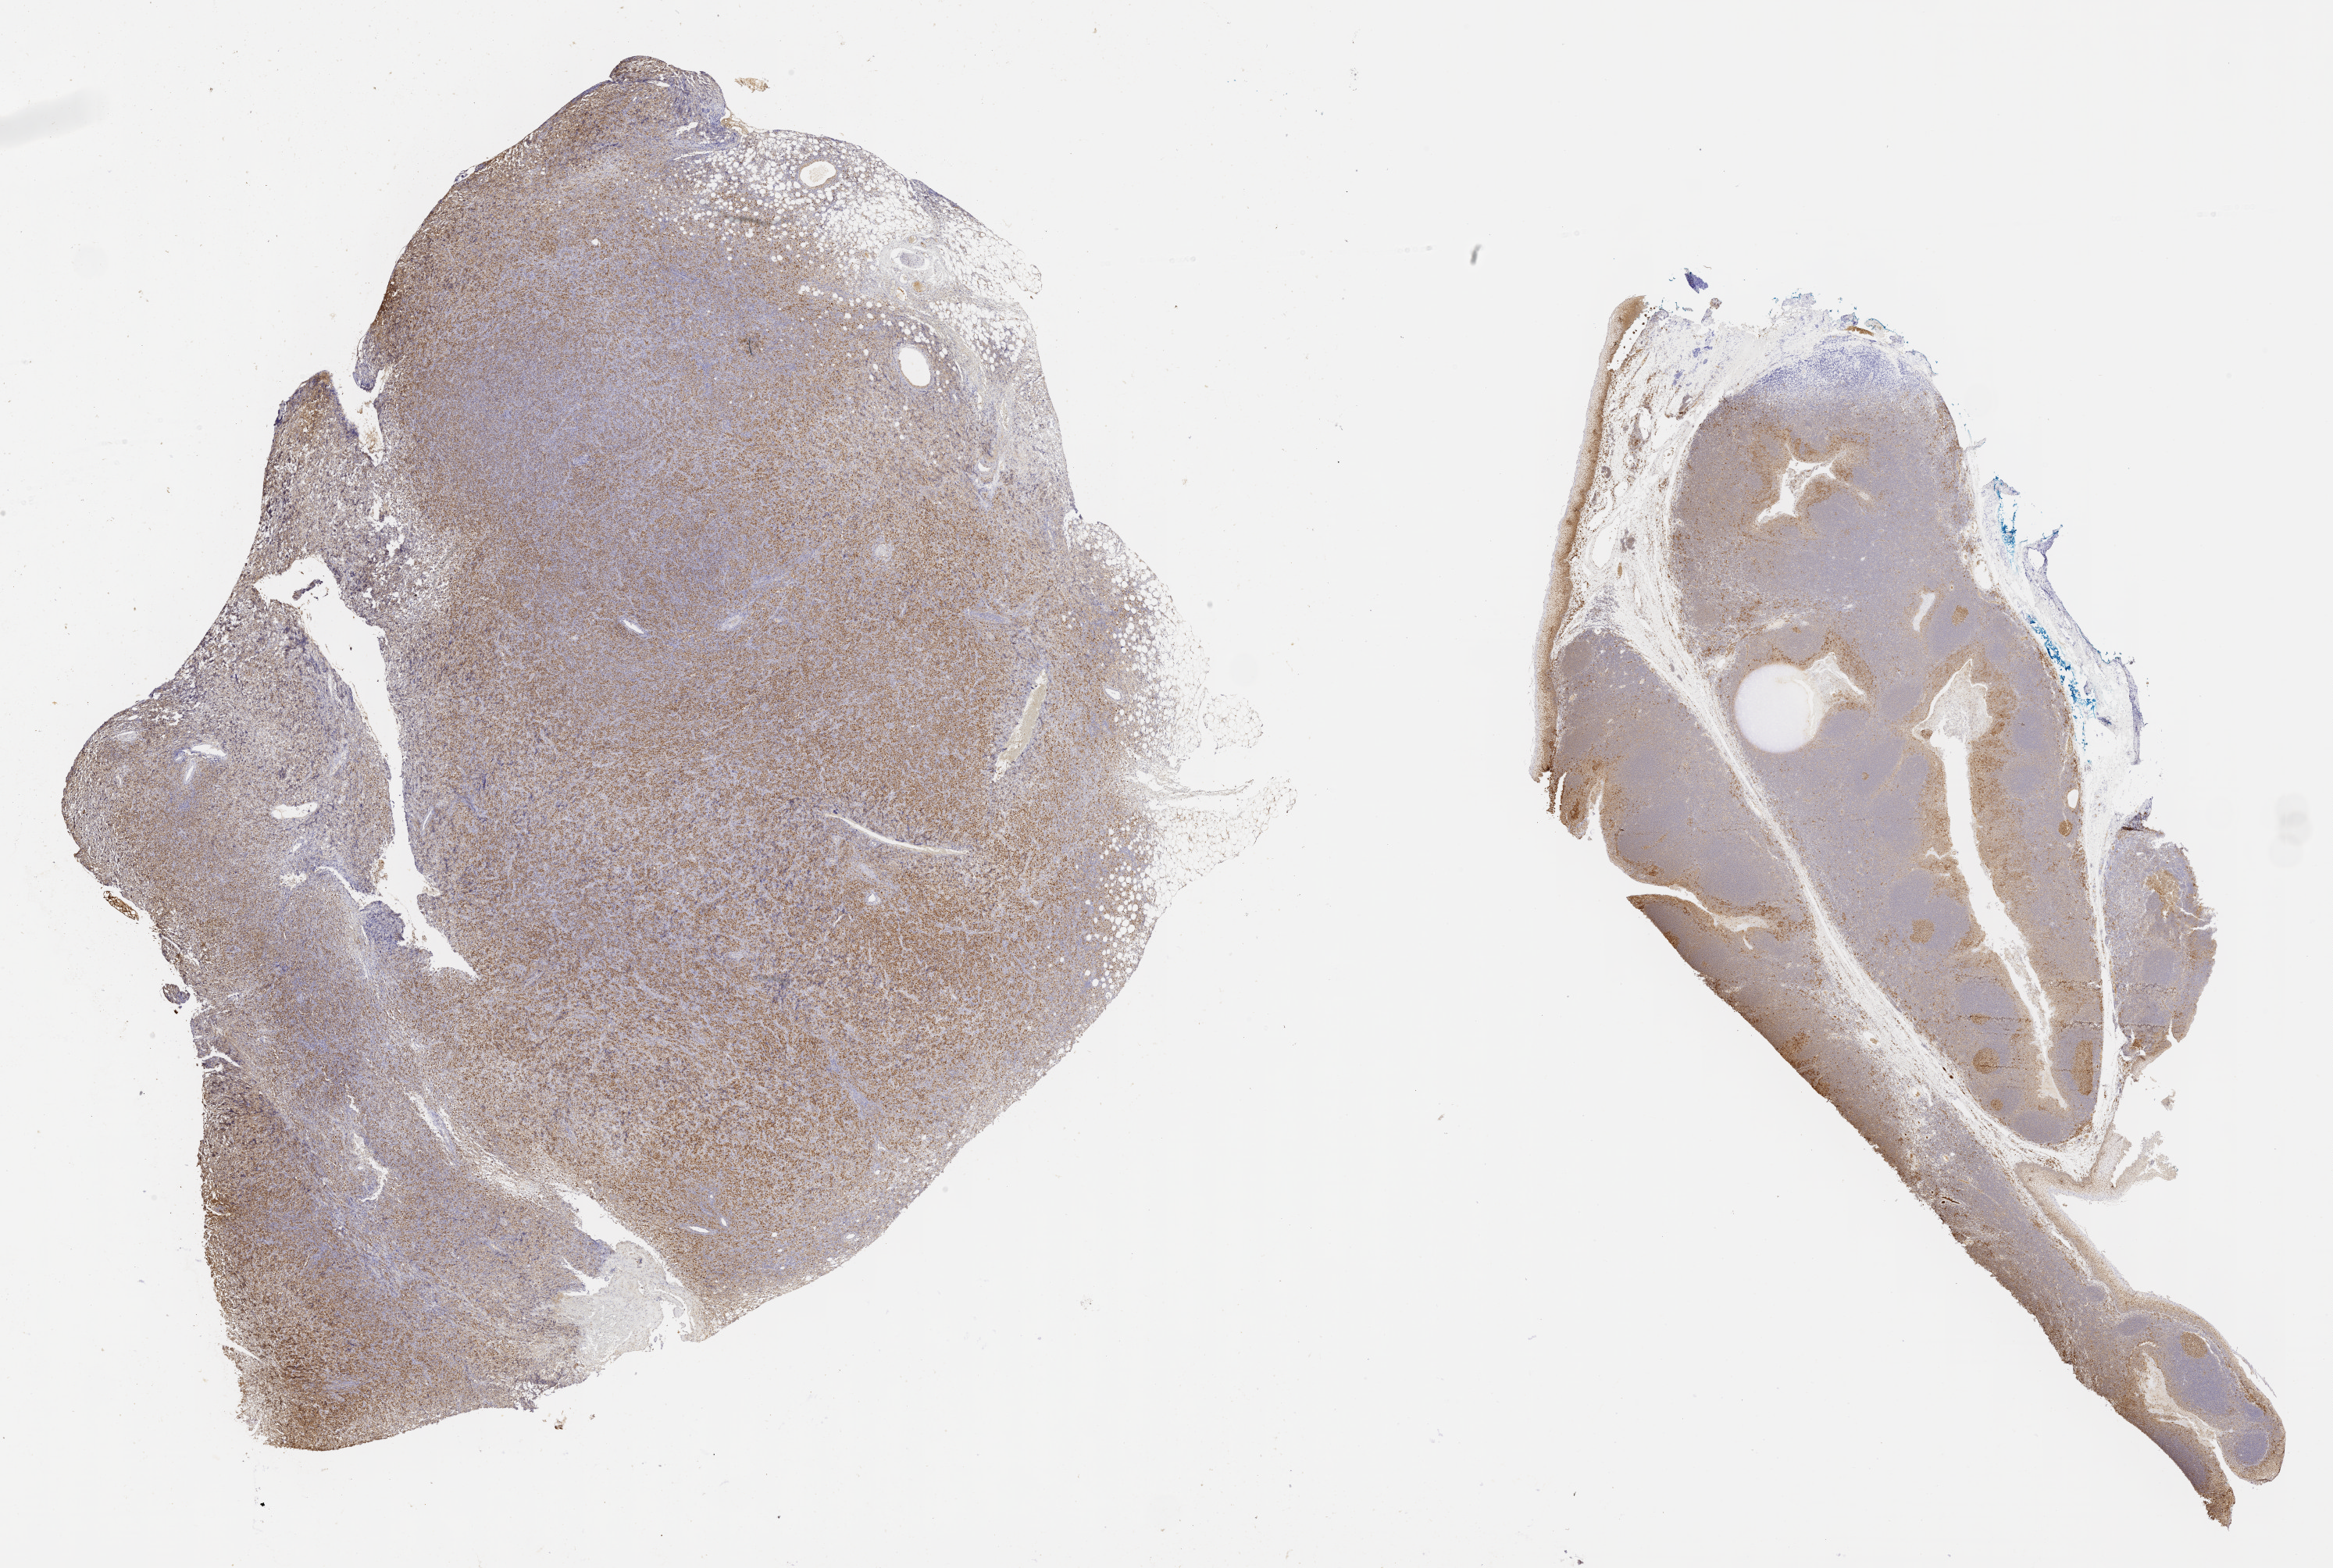
Whole-slide image, immunohistochemical stain for BCL6, whole scanned area (about 24.2 x 16.2 mm) shown as a low-resolution overview. Female patient.
Specimen: tumor tissue.